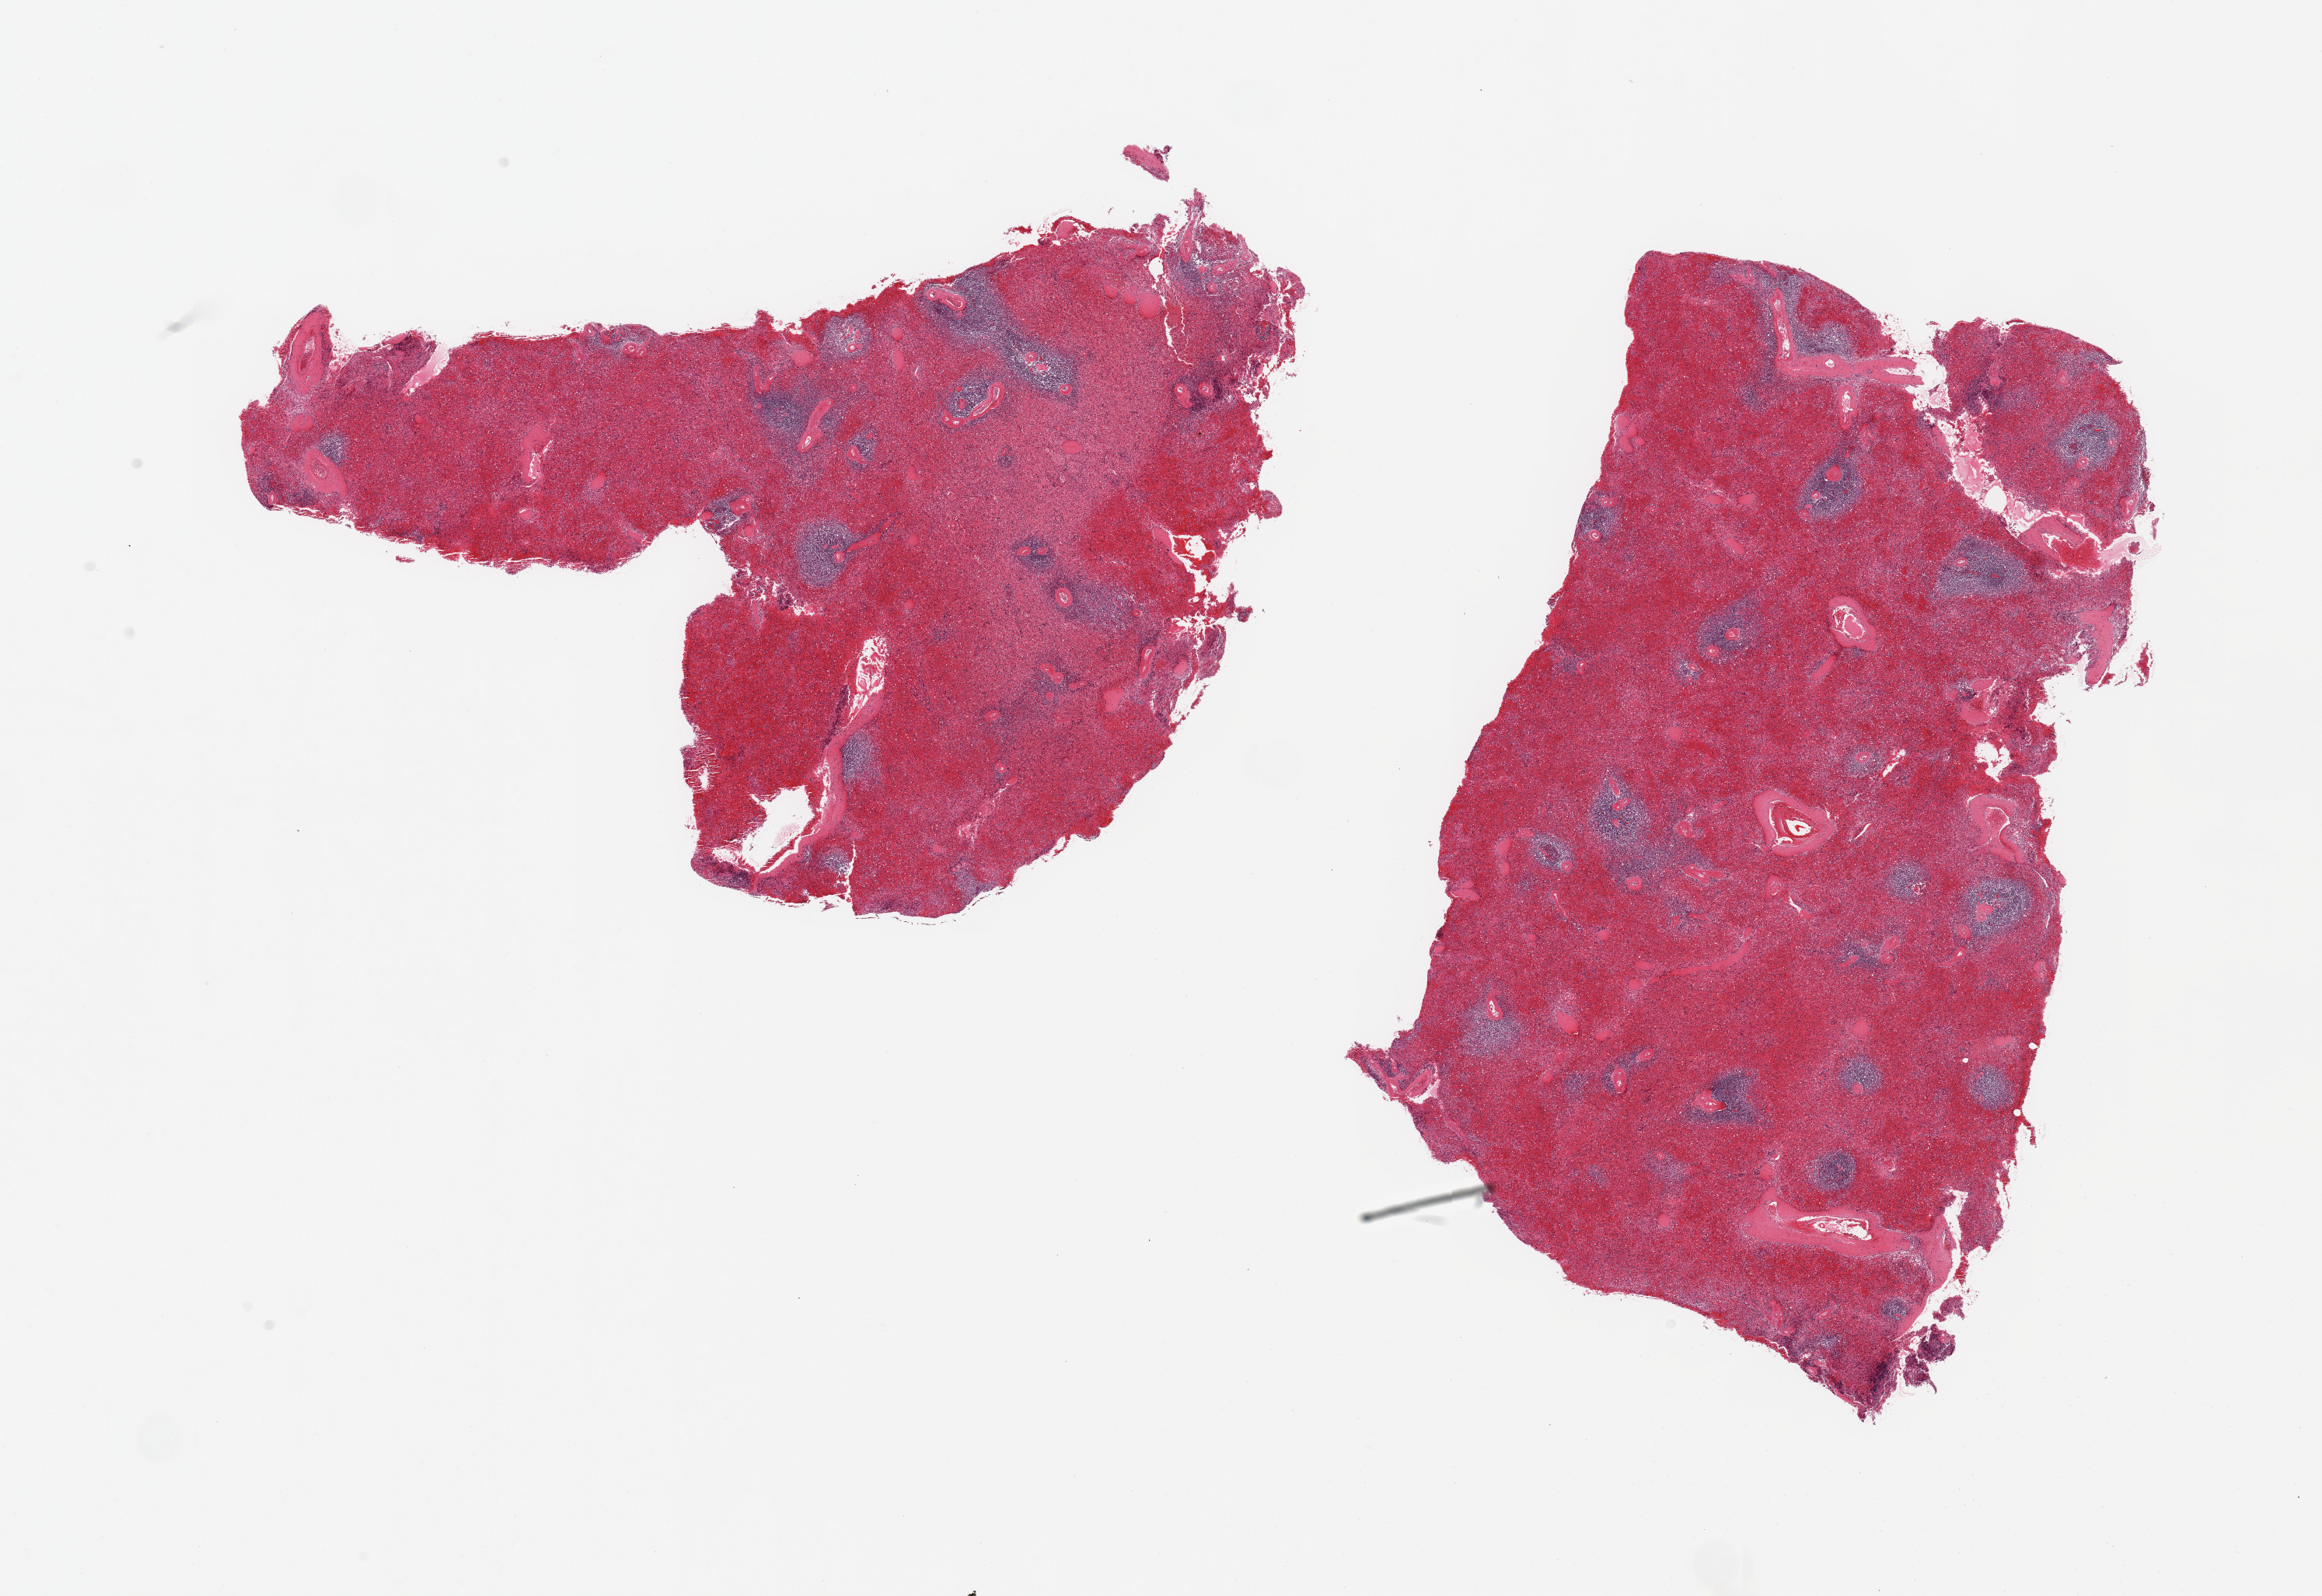
Digitized haematoxylin and eosin-stained section, whole scanned area (about 23.6 x 16.2 mm) shown as a low-resolution overview. PAXgene-fixed, paraffin-embedded tissue. Section of spleen (target tissue). Tissue donor sample. Male donor.
Reviewer comment on this tissue sample: 2 pieces, mild congestion.